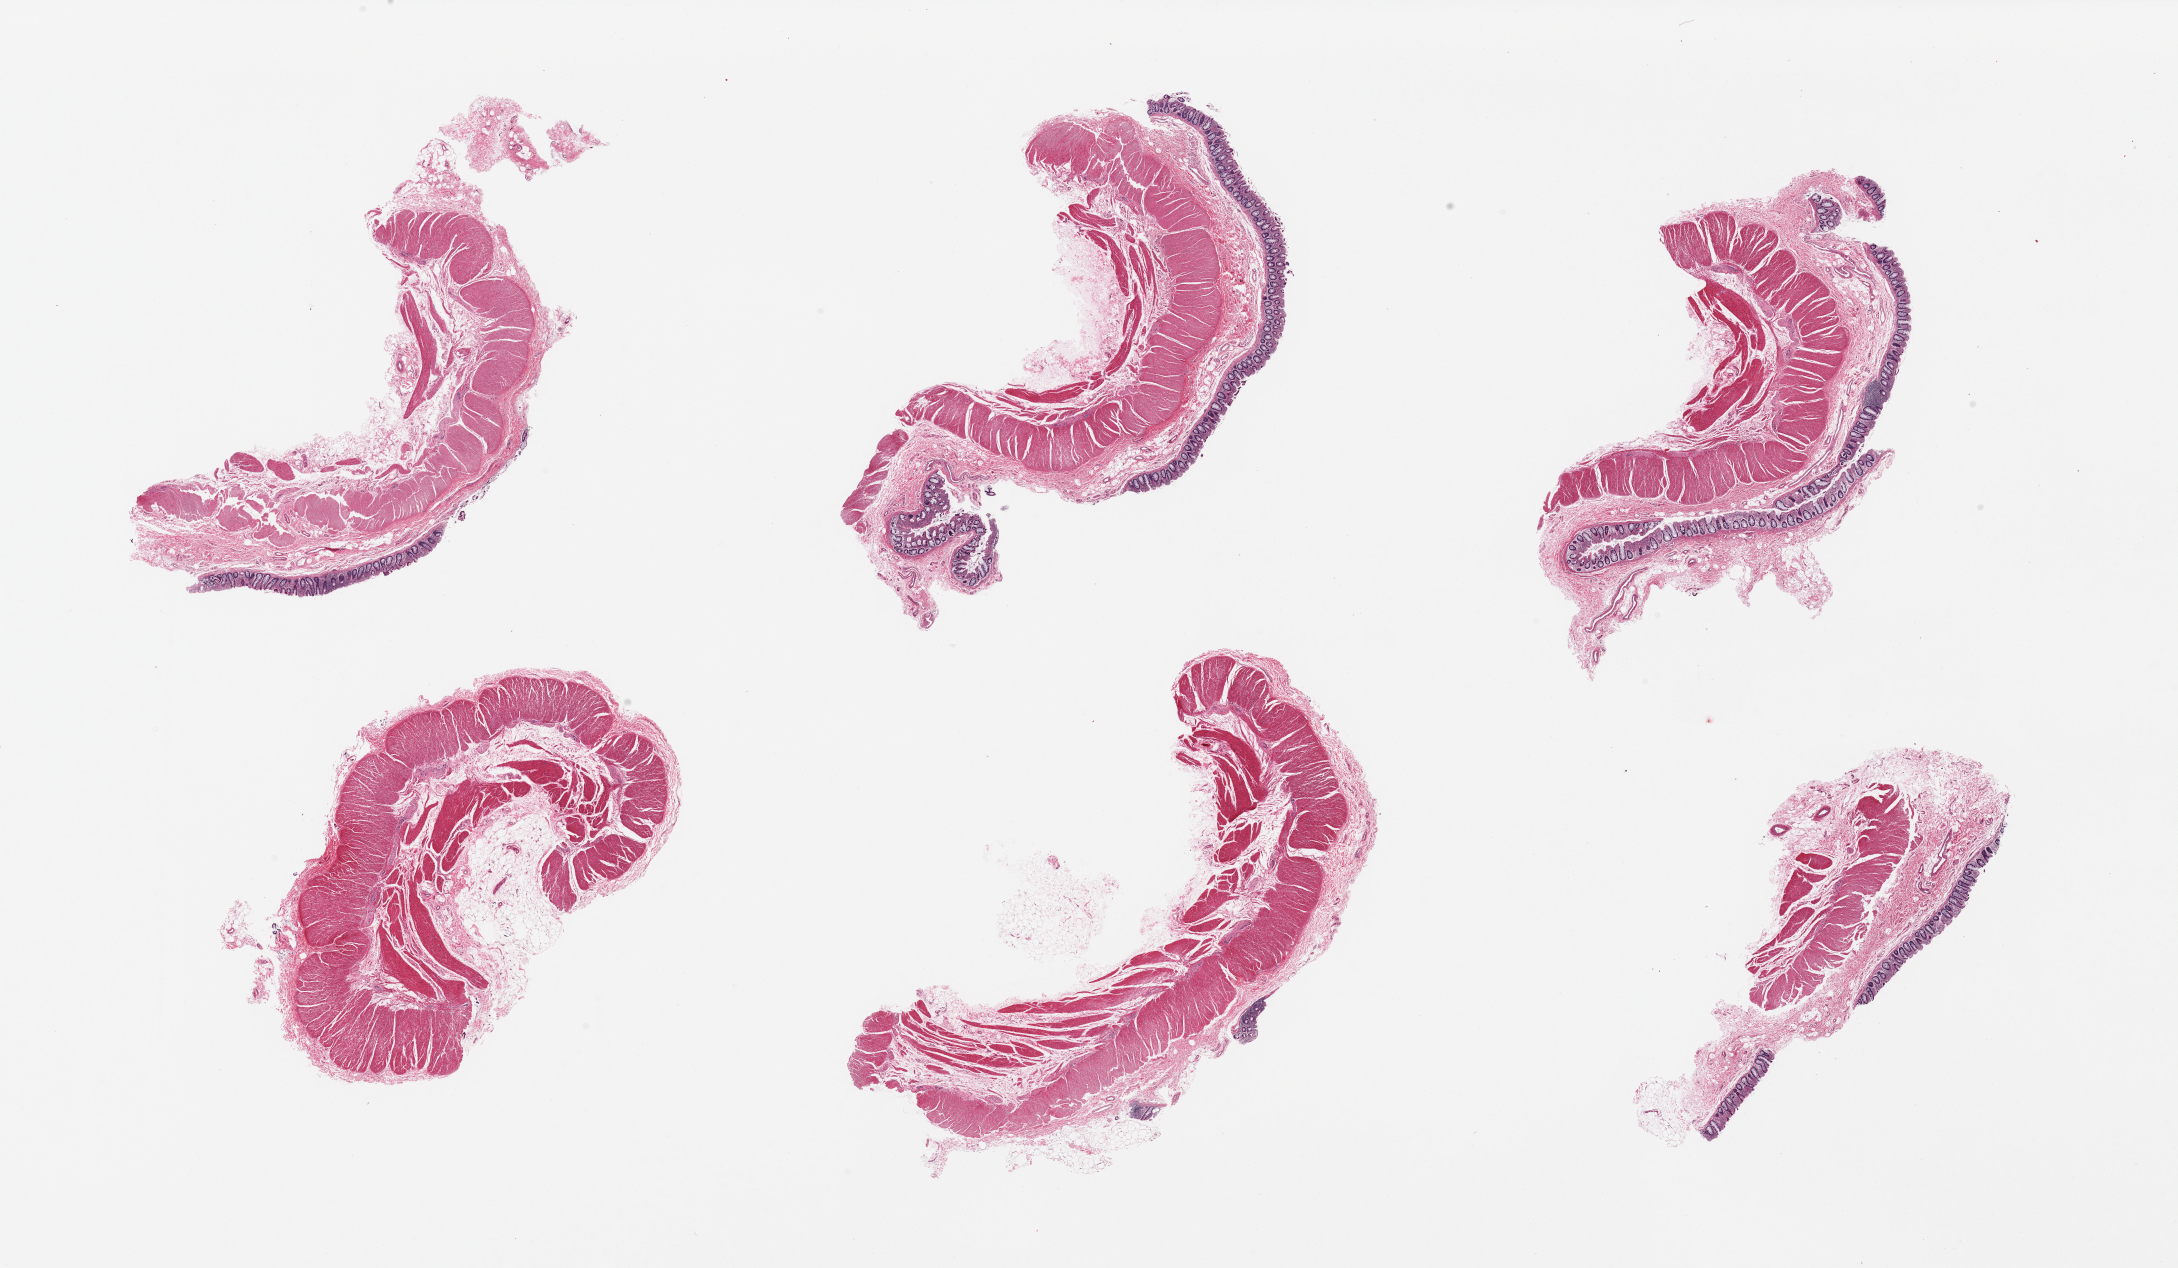
Digitized hematoxylin and eosin (H&E)-stained section, brightfield, a low-resolution overview of the entire scanned area, about 34.5 x 20.1 mm. PAXgene-fixed paraffin-embedded (PFPE) section. Target tissue: sigmoid colon. Donor tissue sample. Donor sex: male.
• review note (as recorded): 6 pieces, NOT prostate as originally labeled. Colon. All contain muscularis (target of sigmoid colon specimen), only one lacks mucosa (not target of sigmoid colon specimen)